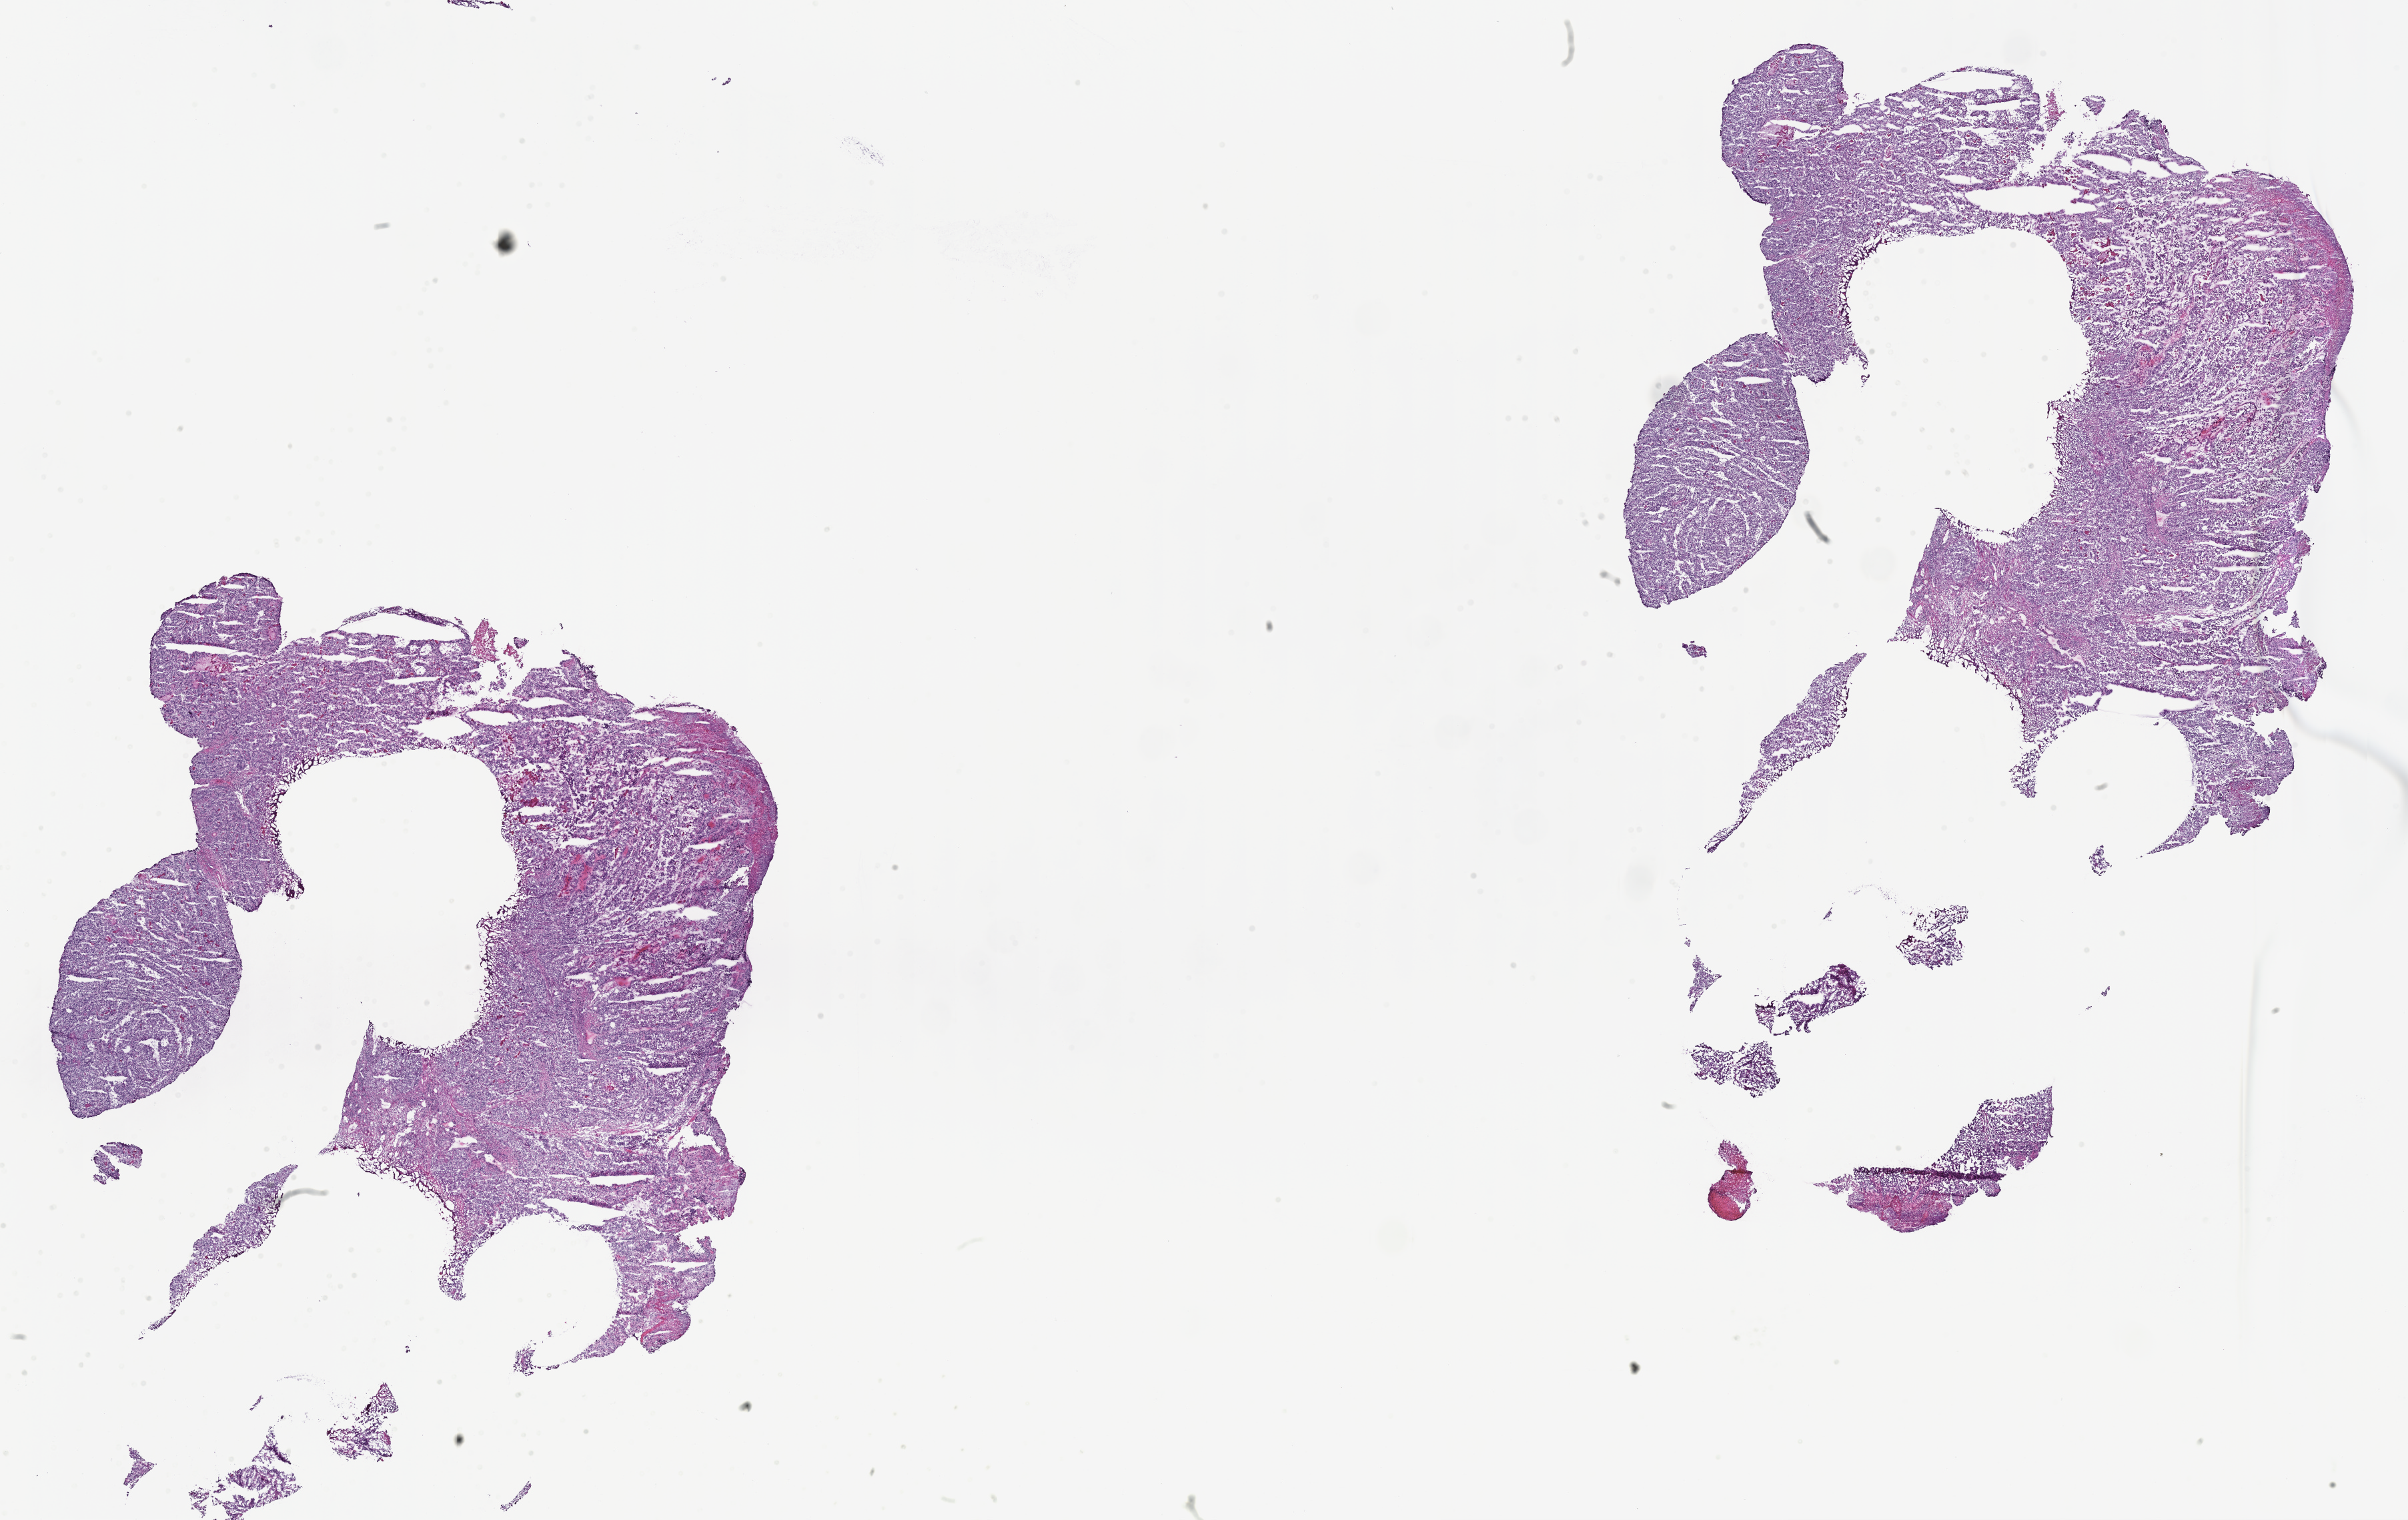
Haematoxylin and eosin whole-slide image, shown as a low-resolution overview of the whole scanned area (about 29.1 x 18.4 mm); frozen section (tissue freezing medium); specimen: primary tumor. Female patient; age at initial diagnosis 75 years. Tumor grade: G3 (poorly differentiated). Composition of this section per pathologist review: tumor cells 85%, tumor nuclei 85%, stromal cells 5%, necrosis 0%, normal cells 10%. Infiltration values recorded for this section: lymphocyte infiltration 5%, monocyte infiltration 0%, neutrophil infiltration 0%.
Diagnosis: Adenocarcinoma, NOS. AJCC pathologic stage: Stage IIB. Section: bottom of the tissue portion.